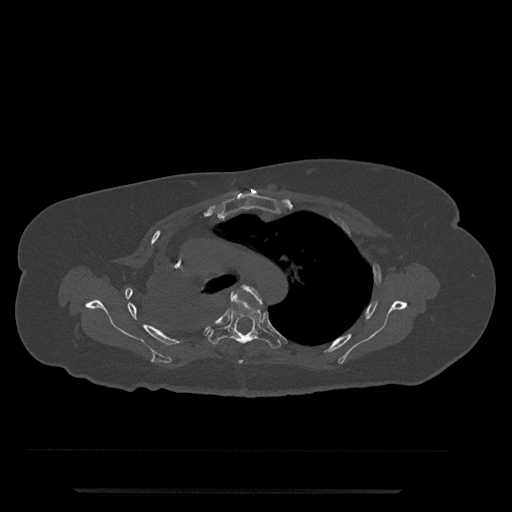
CT including the spine, one axial slice; slice 554 of 797 in the series (ordered by position); bone window (W 1800 / L 400 HU); 0.5 mm slice thickness; 512 × 512 image matrix. Female patient, age 51 years. Case-level facts recorded for this patient, not image findings: primary cancer: neuro; vertebrae with lytic lesions (as recorded): T8.
Outlined on this slice (semi-automatic segmentation, software-assisted and operator-edited):
- T4 vertebra: bounding box <238,285,262,364> (left, top, right, bottom; pixels)
- T5 vertebra: <207,294,281,349>